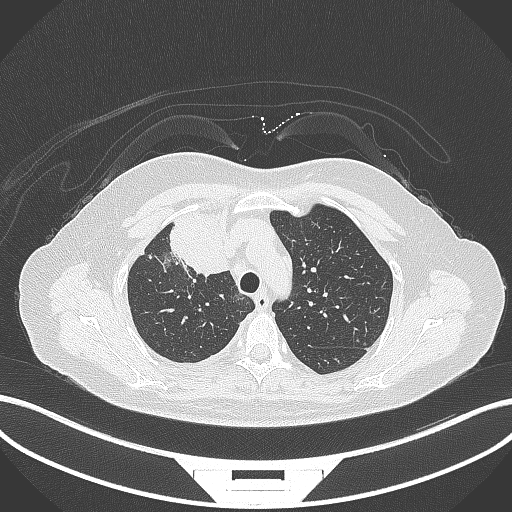
Chest CT, one axial slice. Slice 230 of 305 in the series (ordered by position). 120 kVp. Lung window (W 1500 / L -600 HU). 1 mm slice thickness. 512 × 512 image matrix, field of view 400 × 400 mm. Patient: female, 52 years. From the clinical record (not read from this slice): clinical TNM (as recorded): T3 N1 M1.
Structures marked on this image (bounding box drawn by a radiologist):
- lung tumour (recorded histology: adenocarcinoma): bounding box [x1, y1, x2, y2] px = [163, 209, 230, 278]